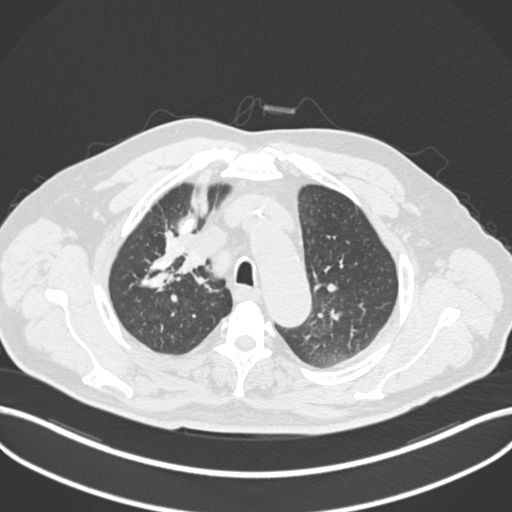
Chest CT, one axial slice. Position 158 of 255 along the scan axis. Reconstruction kernel B30f. Lung window (W 1500 / L -600 HU). 512 × 512 image matrix. Patient: male, 60 years. Case-level facts recorded for this patient, not image findings: clinical TNM (as recorded): T1b N1 M0.
Annotated regions visible in this slice (rectangle marked by the reading radiologist):
- lung tumour (recorded histology: squamous cell carcinoma): bounding box <168,245,212,291> (left, top, right, bottom; pixels)